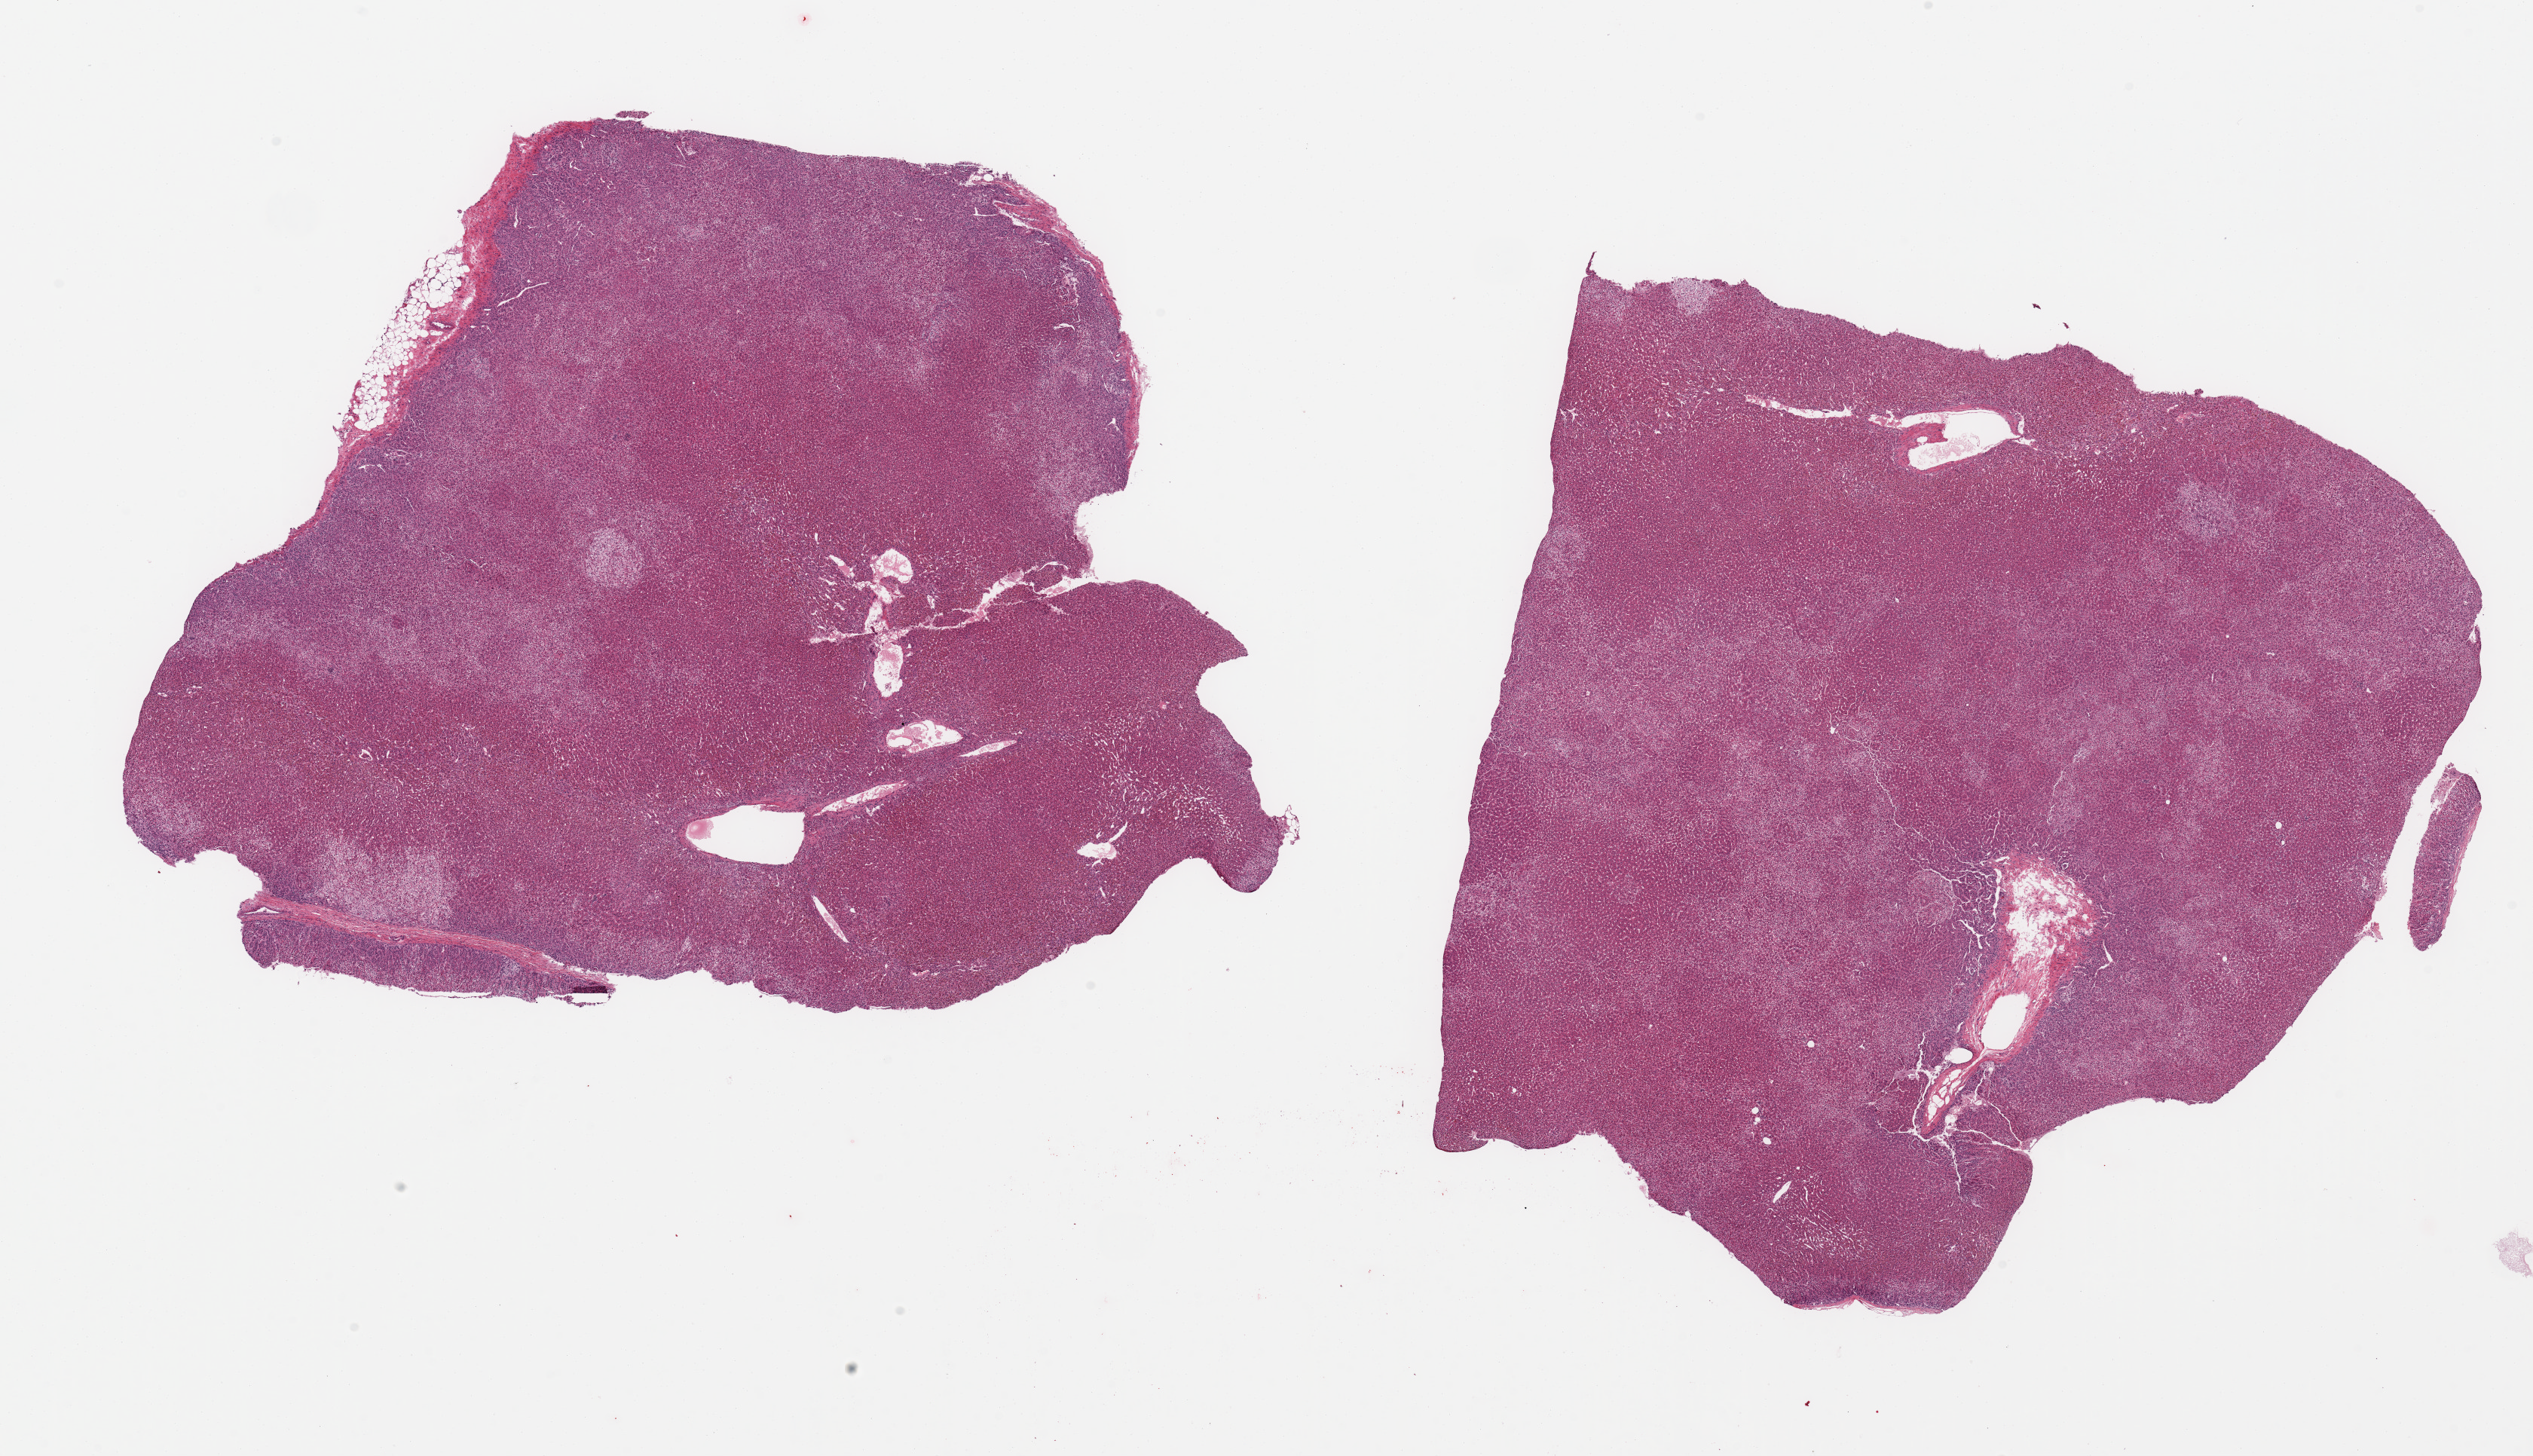
Whole-slide image, H&E stain, brightfield — shown as a low-resolution overview of the whole scanned area (about 26.6 x 15.3 mm), PAXgene-fixed, paraffin-embedded tissue, section of adrenal gland (target tissue), tissue donor sample. Donor: male.
* reviewer comment on this tissue sample: 2 pieces; predominantly adrenal cortex, trivial component of attached fat